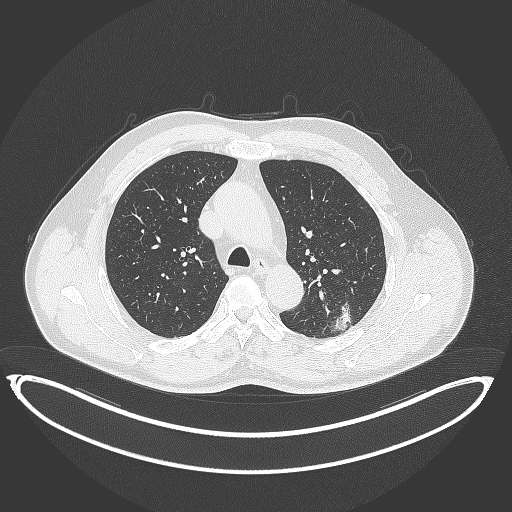
Chest CT, one axial slice; position 253 of 399 along the scan axis; reconstruction kernel B70f; 120 kVp; lung window (W 1500 / L -600 HU); 1 mm slice thickness; 512 × 512 image matrix, field of view 469 × 469 mm. Male patient, age 58 years. From the clinical record (not read from this slice): clinical TNM (as recorded): T1c N0 M0.
Outlined on this slice (rectangle marked by the reading radiologist):
- lung tumour (recorded histology: adenocarcinoma): bounding box <330,295,355,333> (left, top, right, bottom; pixels)